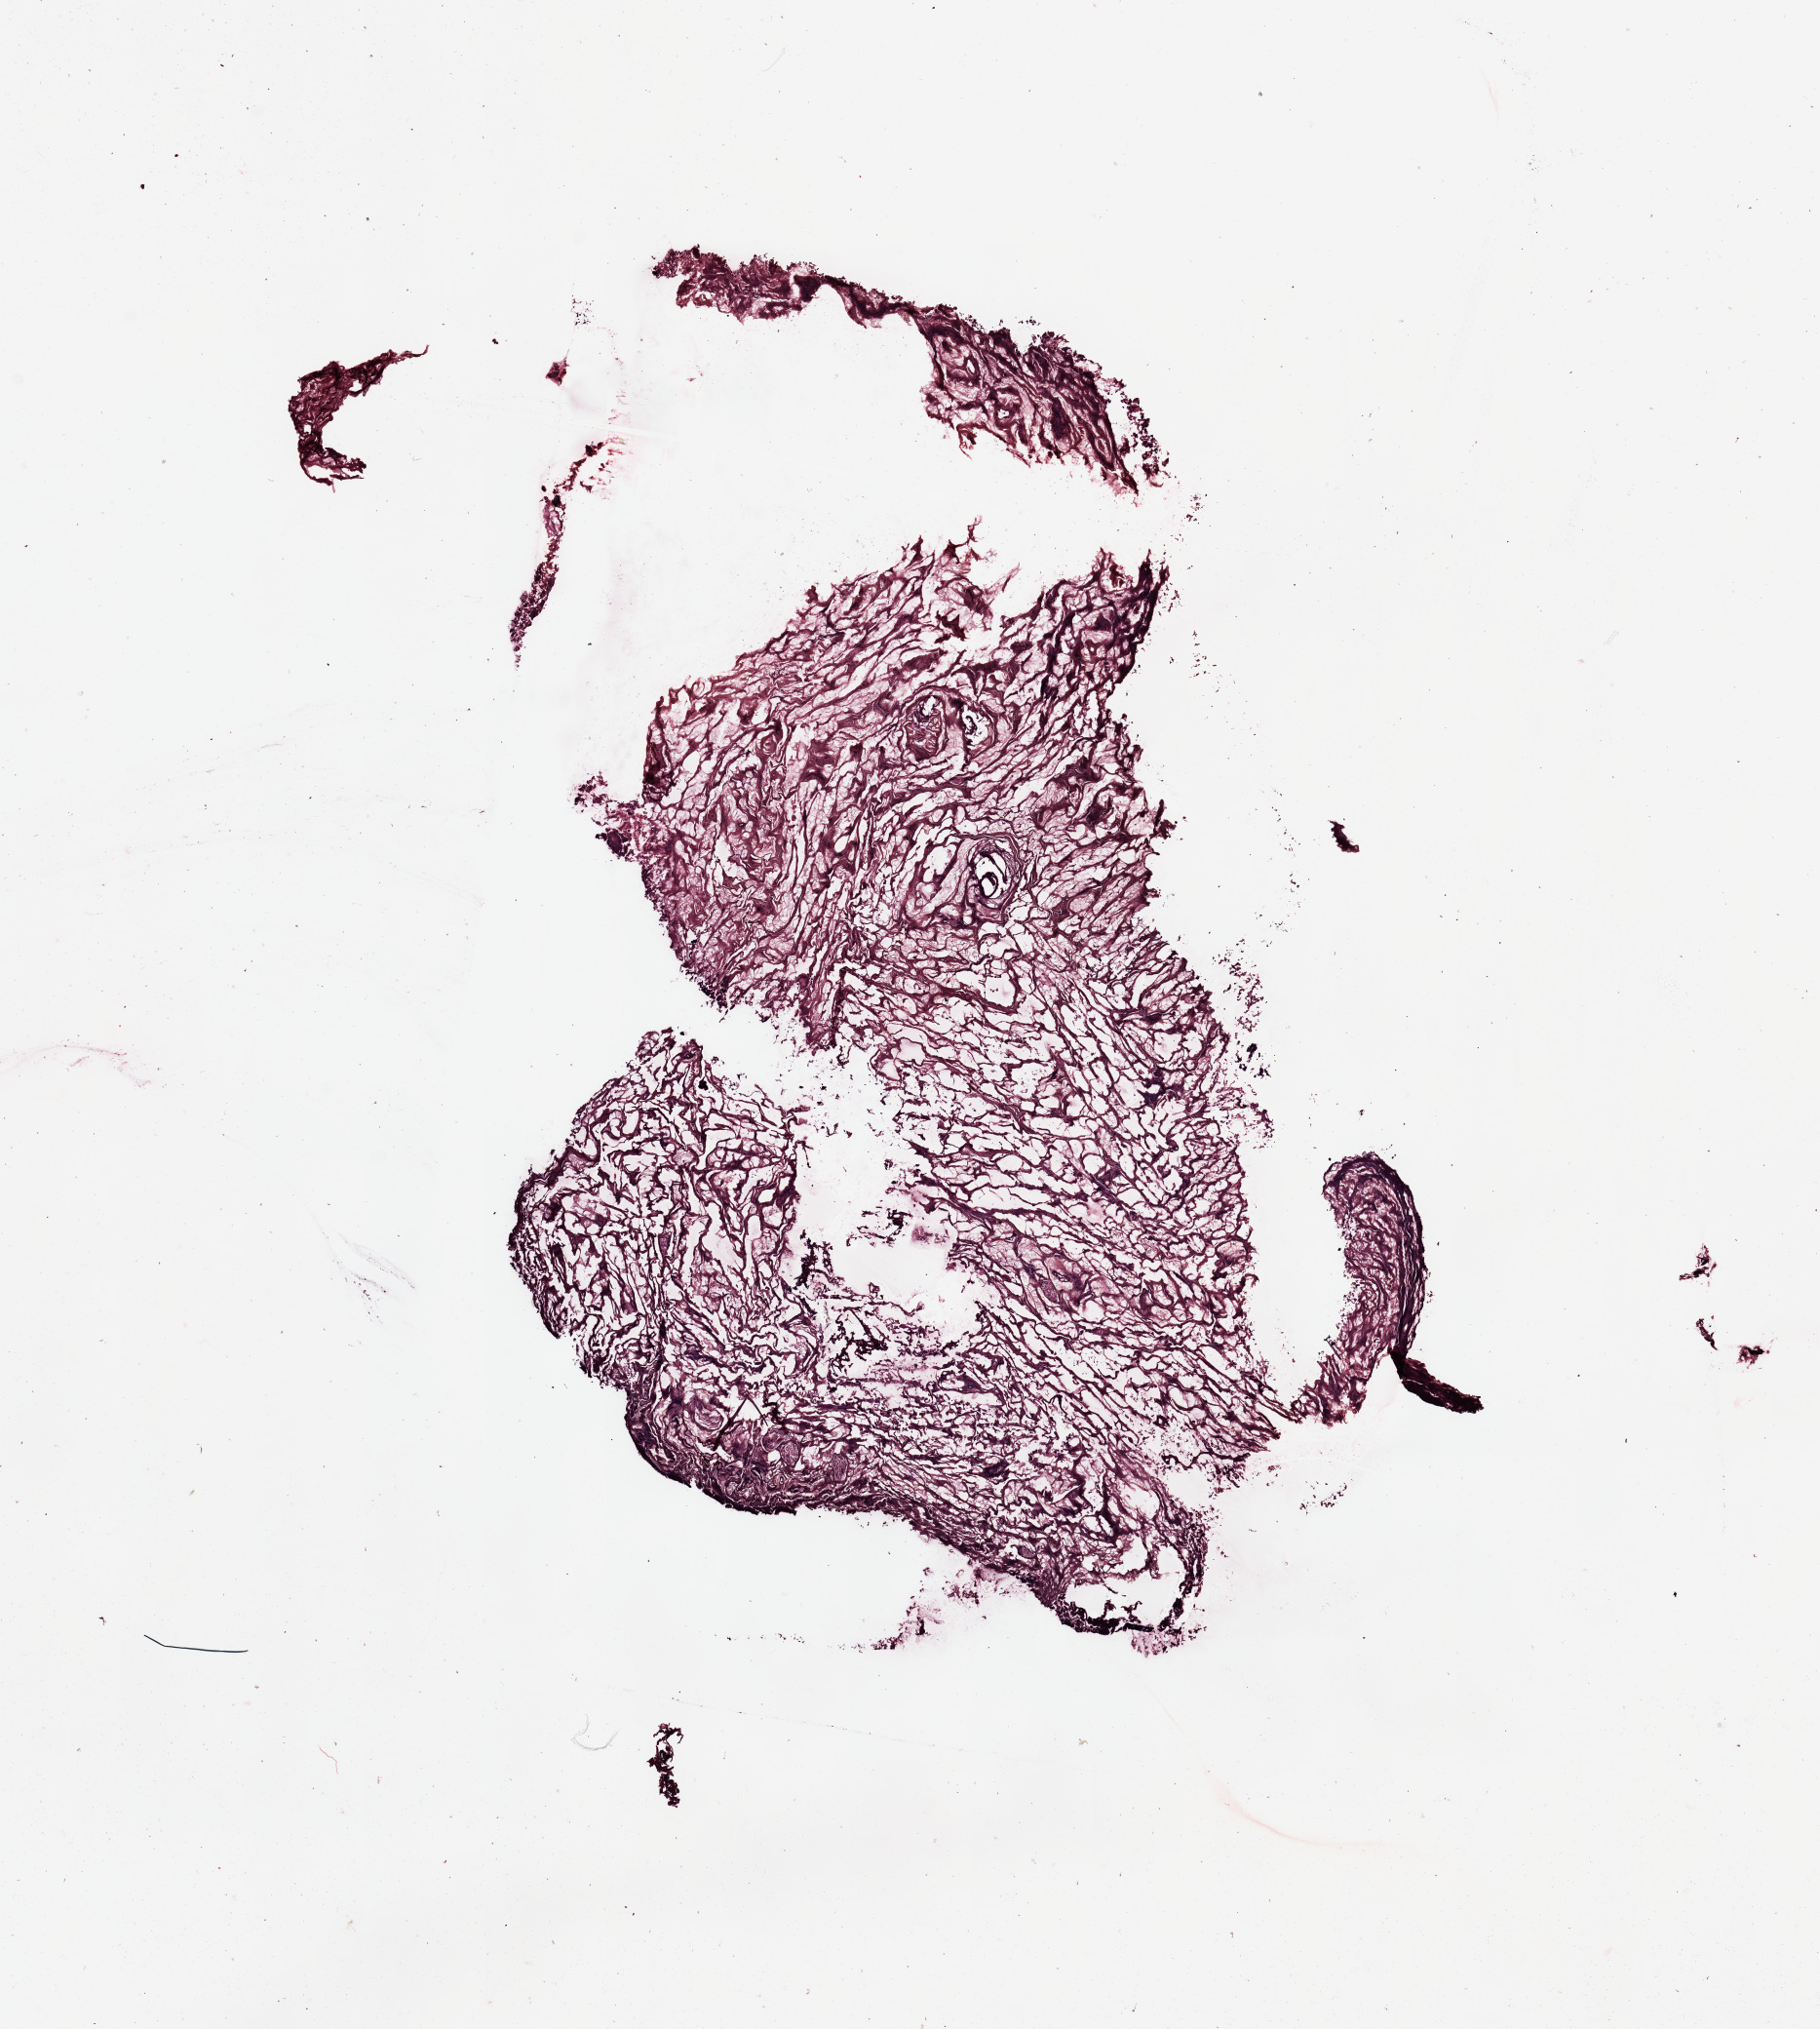
Hematoxylin and eosin (H&E) stained whole-slide image, low-resolution overview of the scanned area, about 14.8 x 16.5 mm (from a 20x scan); uterus, normal (non-tumour) tissue. Patient: female, age 78 years.
This section: normal (non-tumour) tissue from the same patient. Patient diagnosis: Endometrioid adenocarcinoma, NOS.